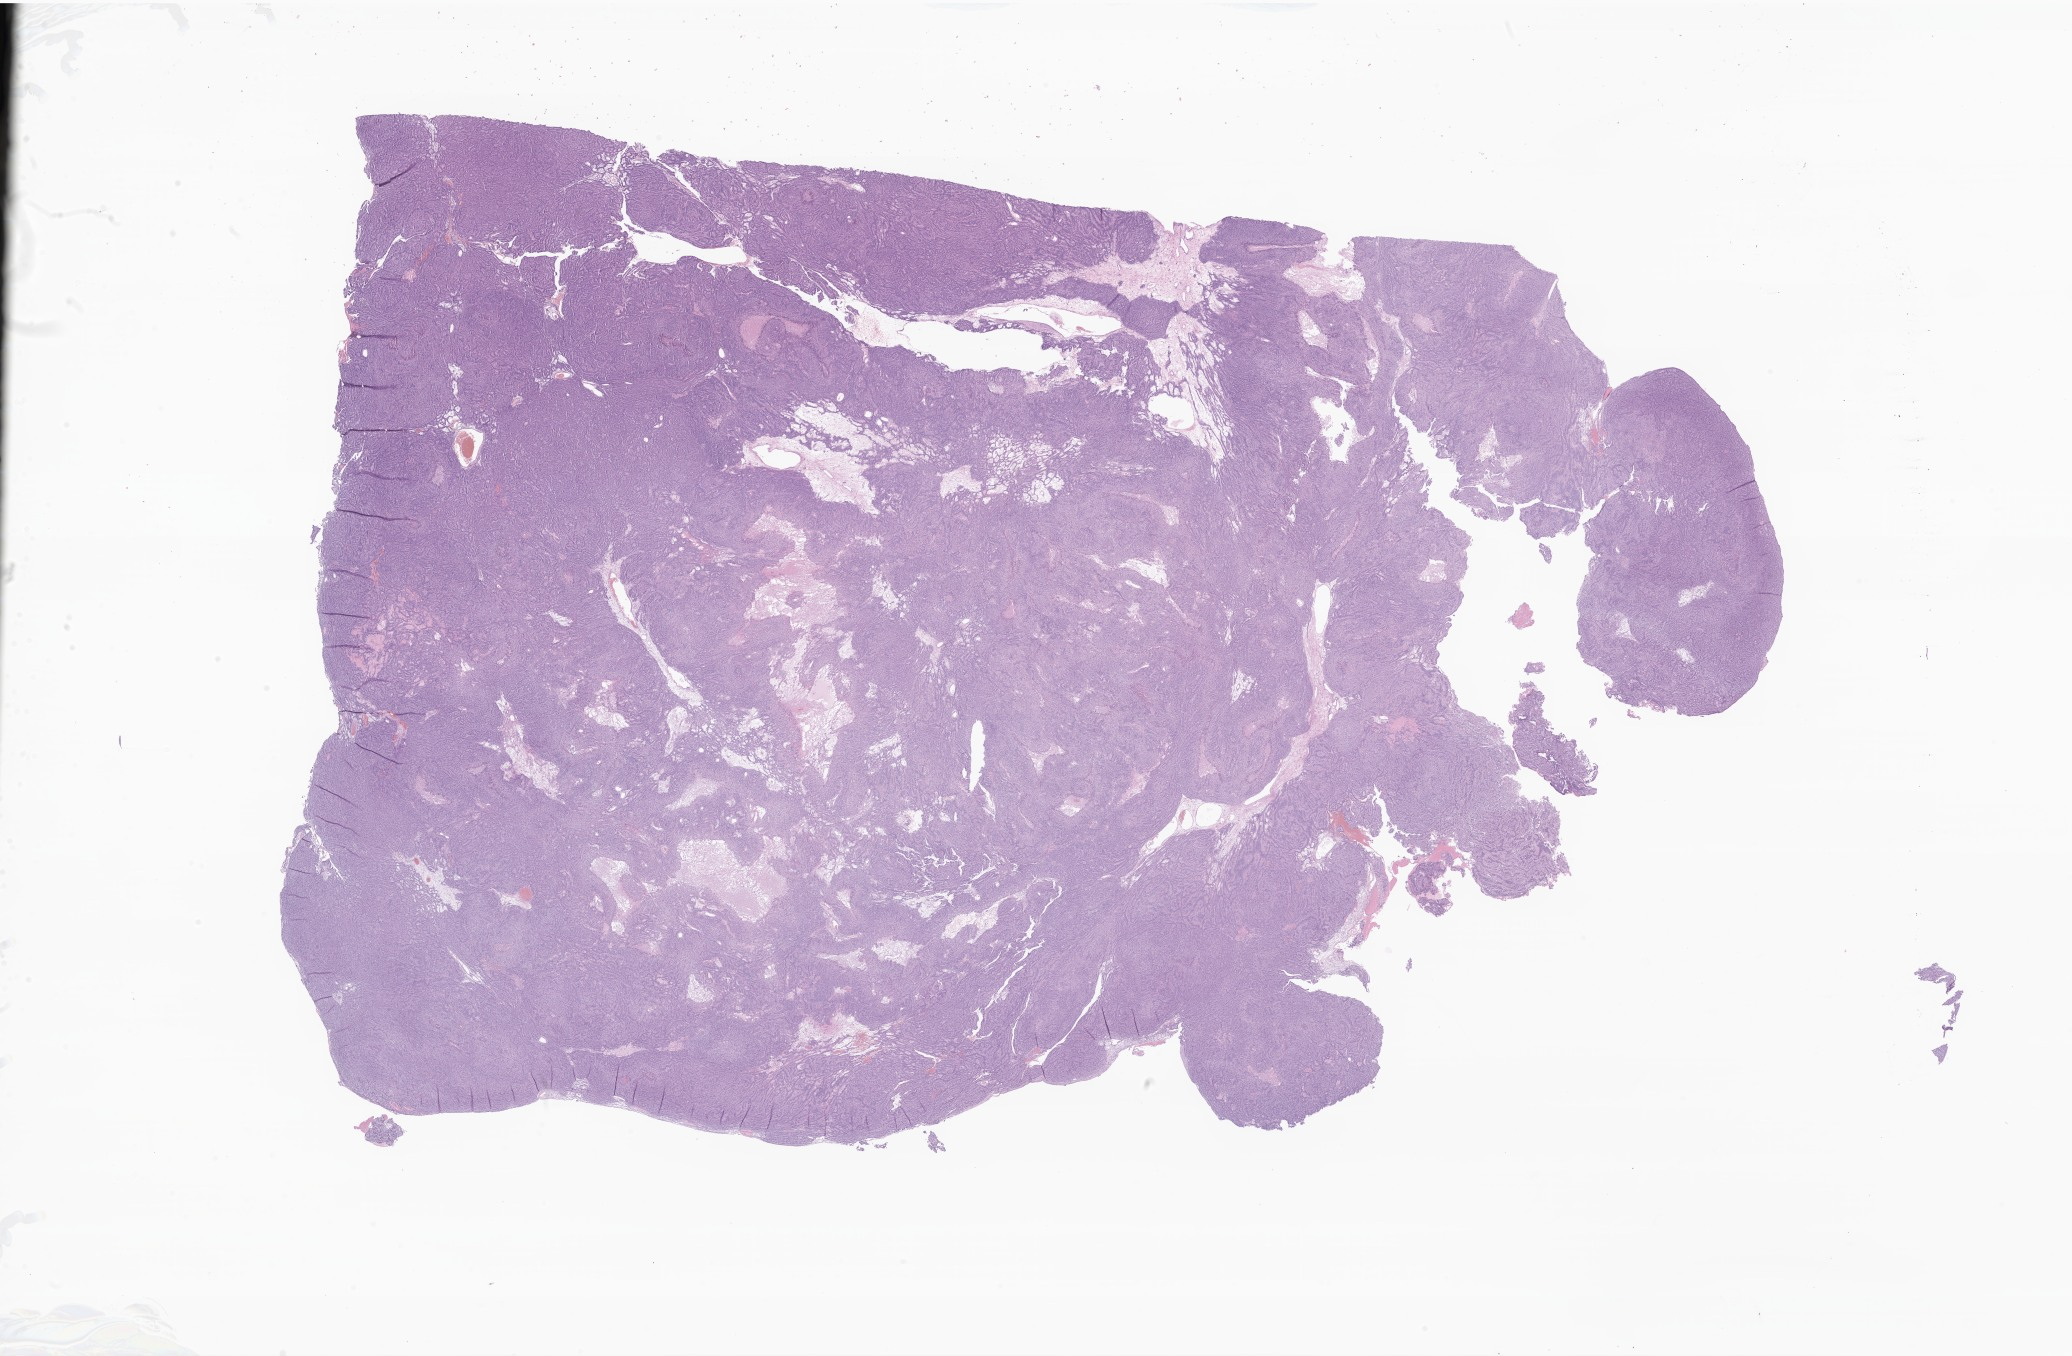
Whole-slide image, H&E stain of tumor tissue from the brain — low-resolution overview of the scanned area, about 35.0 x 22.9 mm. Formalin-fixed paraffin-embedded section. Patient female; age 60 months (5 years).
Recorded diagnosis: Neoplasm, malignant.